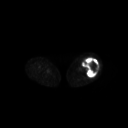
FDG PET of an extremity soft-tissue mass (from a PET/CT study), one axial slice. 3.27 mm slice thickness. 128 × 128 image matrix, field of view 700 × 700 mm. Patient: female, 62 years. Case-level facts recorded for this patient, not image findings: histological type: undifferentiated – high grade; grade: high; site of the primary tumour: left thigh.
Outlined on this slice (expert contour drawn on MRI and transferred to this co-registered scan by the dataset authors):
- gross tumour volume including surrounding oedema: bounding box [x1, y1, x2, y2] px = [82, 58, 99, 77]
- gross tumour volume (mass): [82, 58, 99, 77]